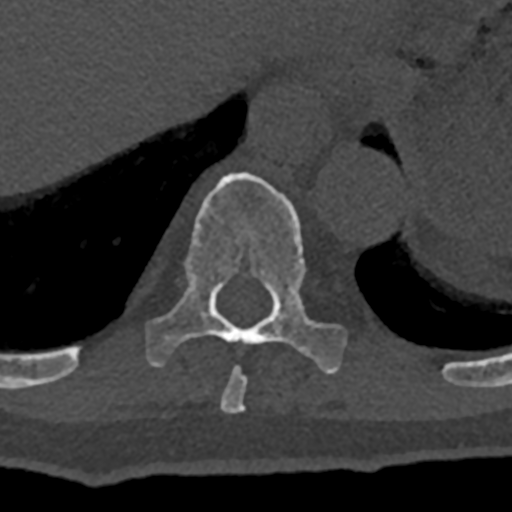
CT including the spine, one axial slice. Position 607 of 797 along the scan axis. Bone window (W 1800 / L 400 HU). 512 × 512 image matrix. Male patient, age 74 years. From the clinical record (not read from this slice): primary cancer: renal; vertebrae with lytic lesions (as recorded): T10, L1, L2, L3, L4, L5.
Outlined on this slice (semi-automatically segmented with operator editing):
- T10 vertebra: bounding box (x1, y1, x2, y2) in pixels: (70, 172, 346, 374)
- T9 vertebra: (220, 366, 247, 413)